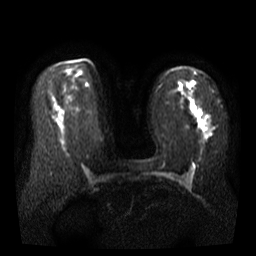
Breast MRI, one axial slice. Slice 25 of 41 in the series (ordered by position). Diffusion-weighted series; image 2 of 4 stored at this slice position (different b-values; order by instance number). 3 T. 5 mm slice thickness. 256 × 256 image matrix, field of view 340 × 340 mm. Female patient.
Structures marked on this image (expert manual segmentation):
- tumour on diffusion-weighted imaging: bounding box [x1, y1, x2, y2] px = [193, 107, 206, 131]